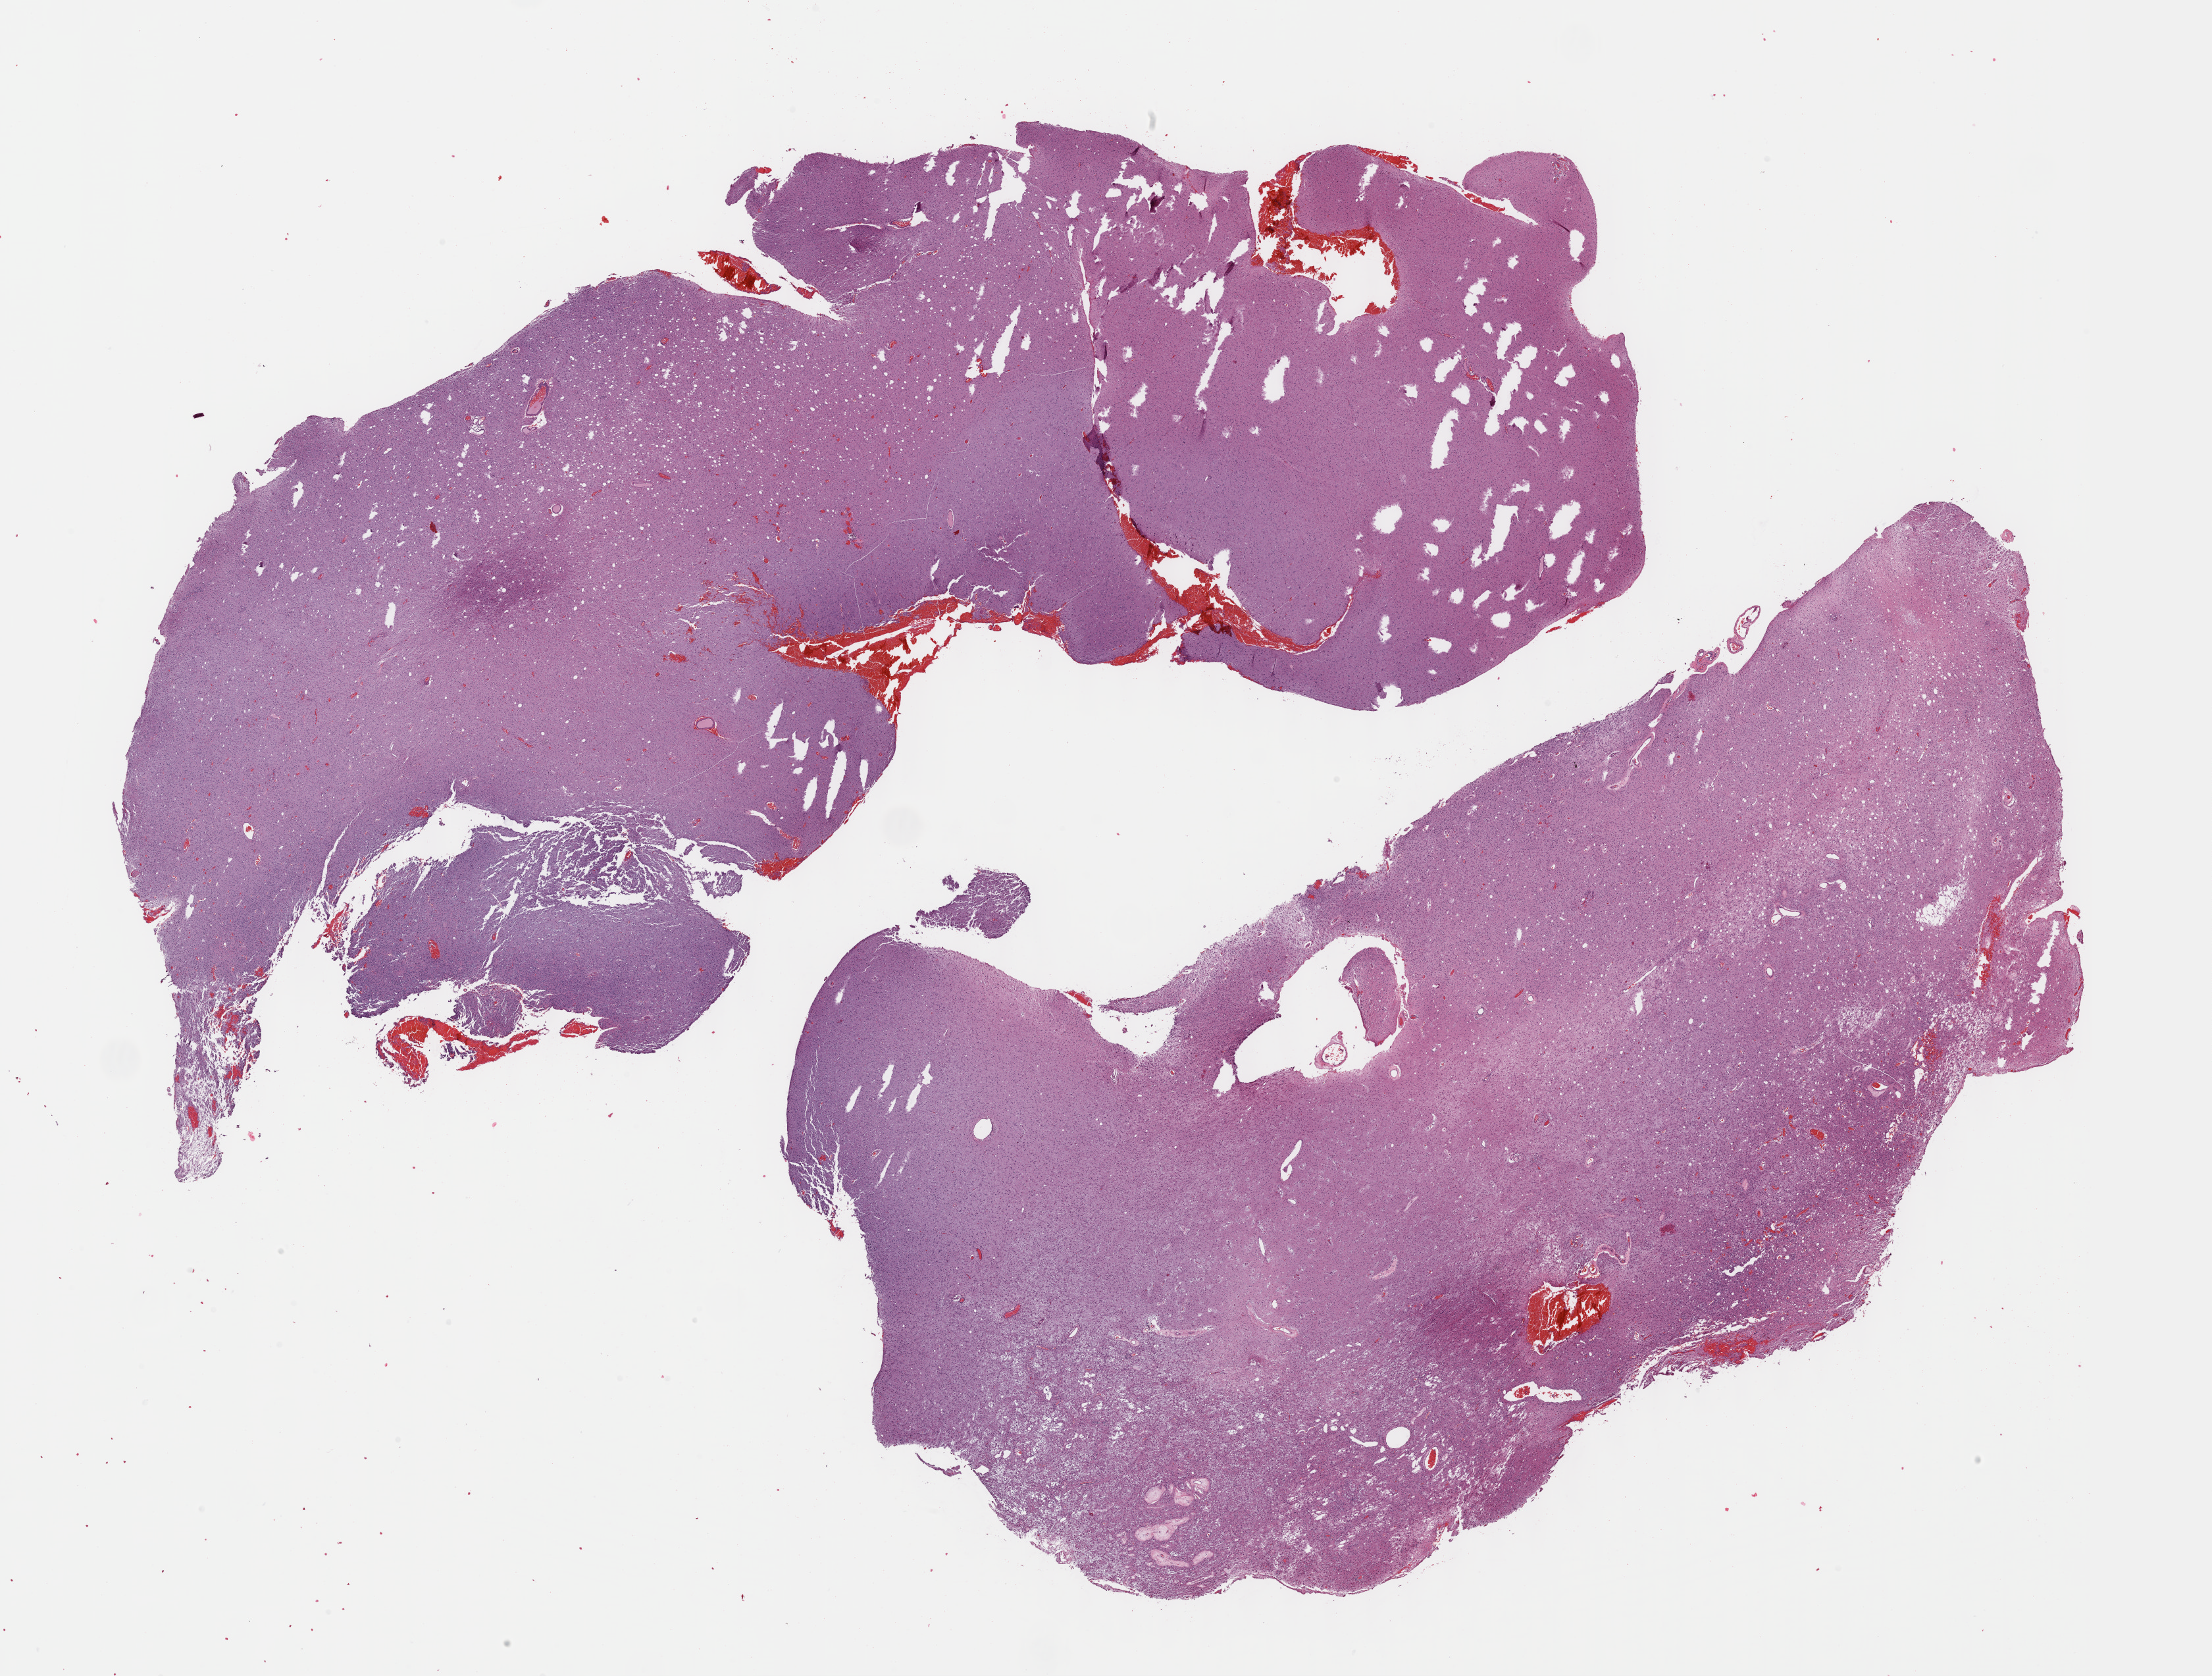
Digitized Hematoxylin and eosin (H&E) stained tissue section (whole slide), a low-resolution overview of the entire scanned area, about 27.2 x 20.6 mm (slide scanned at 40x); formalin-fixed paraffin-embedded (FFPE) diagnostic section; brain, primary tumour sample. Patient: male, age at initial diagnosis 58 years.
Pathologic diagnosis: Mixed glioma (cerebrum).